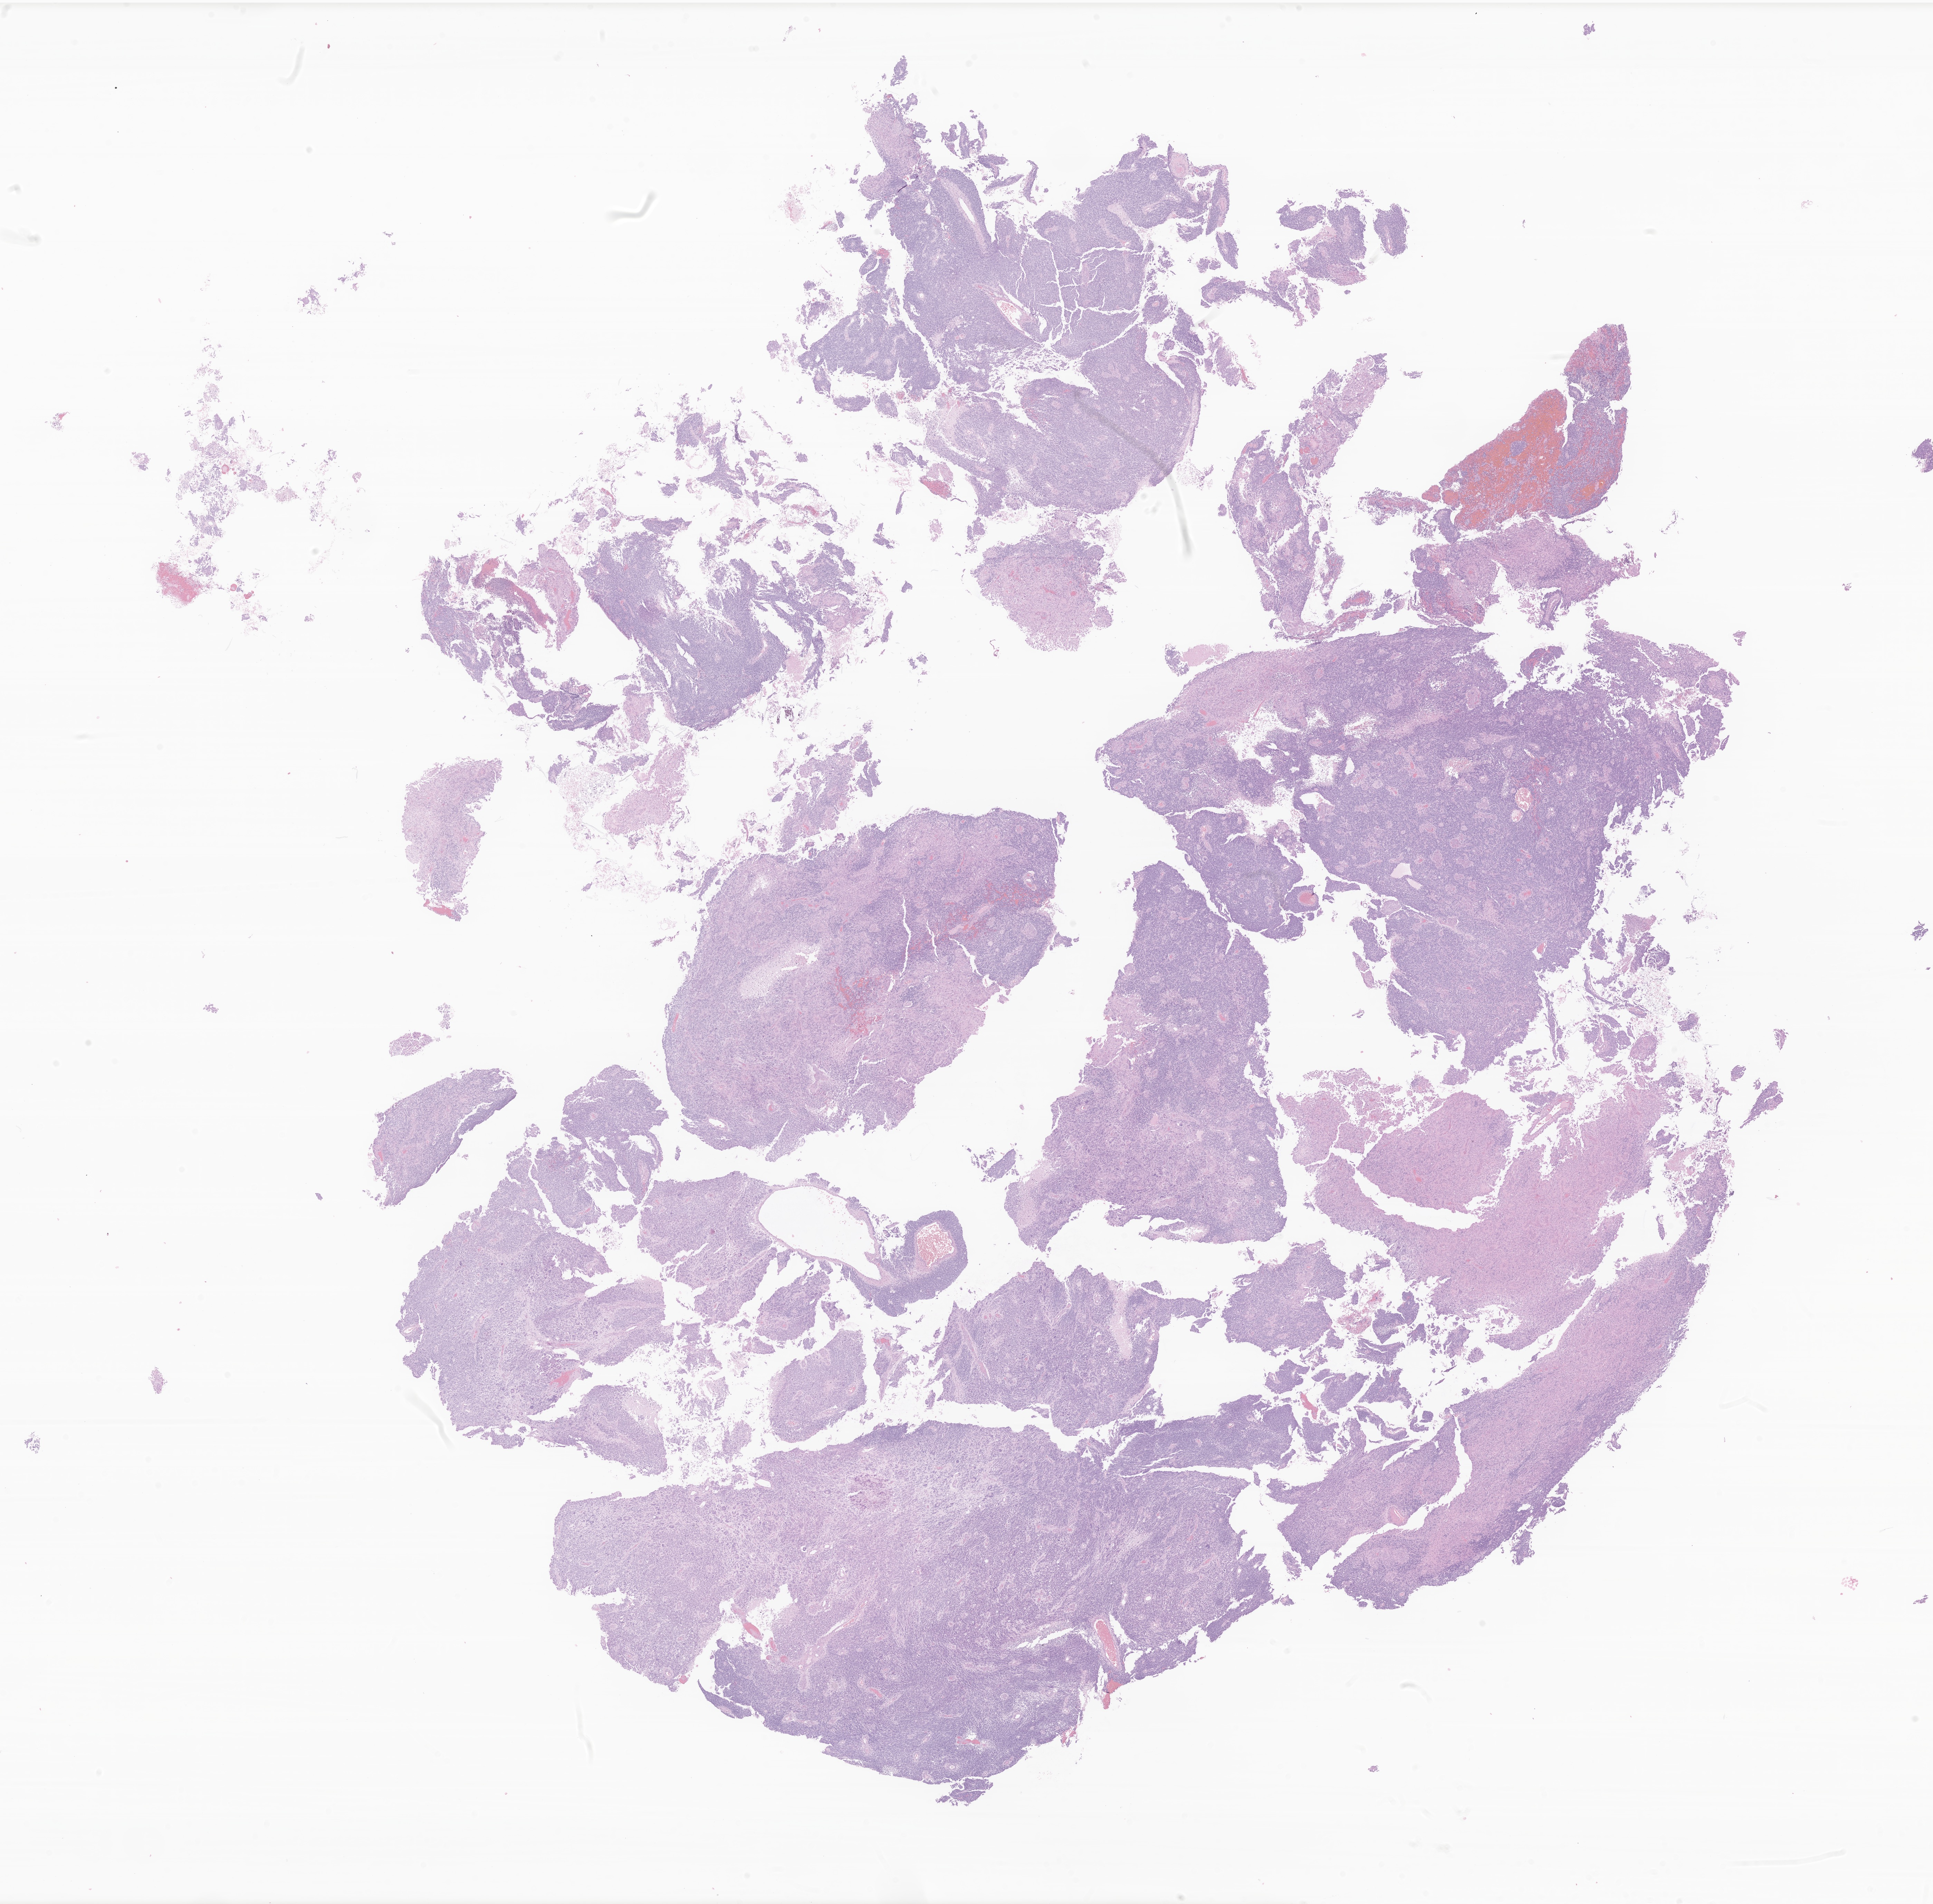
Digitized H&E-stained section of tumor tissue from the temporal lobe — low-resolution overview of the scanned area, about 23.6 x 23.2 mm; formalin-fixed, paraffin-embedded (FFPE) tissue. Male patient, age 95 months (7 years 11 months).
* diagnosis: Glioma, malignant